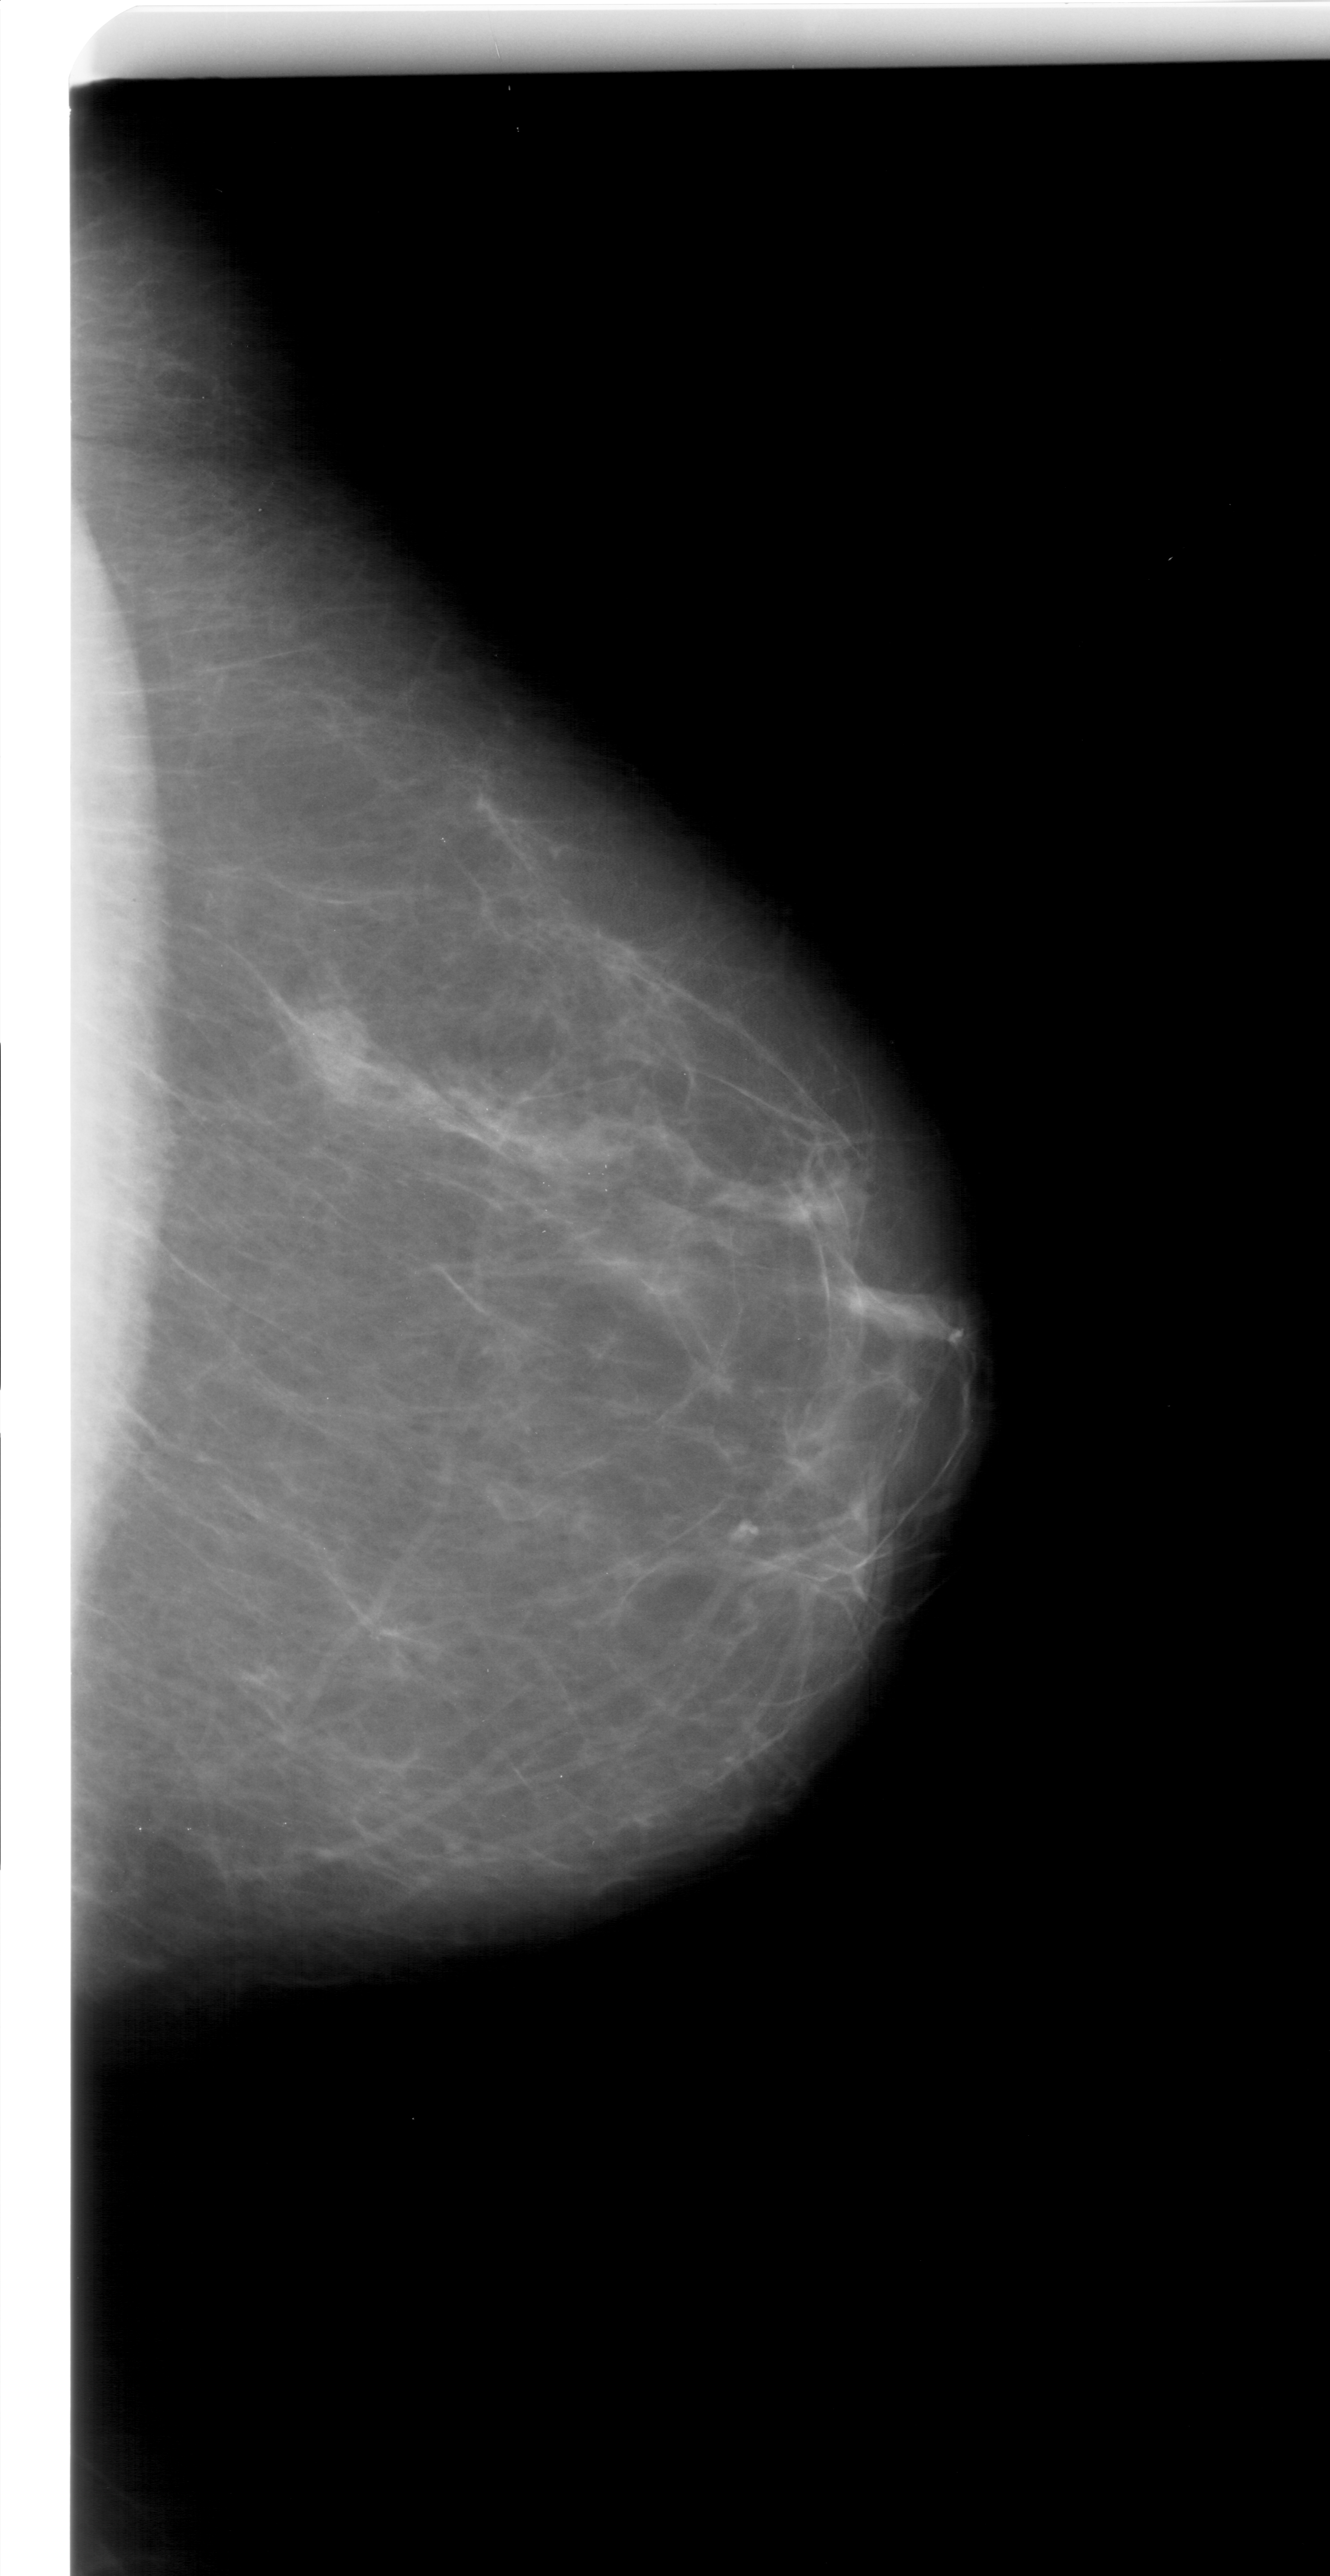
Scanned film-screen mammogram; right breast; craniocaudal (CC) view; BI-RADS breast density category 2 (scale 1–4); 1330 × 2576 image matrix.
Expert-marked regions of interest on this image (one box per marked abnormality):
- mass, shape focal asymmetric density, margins ill defined; BI-RADS assessment category 4; pathology (as recorded): benign: bounding box [x1, y1, x2, y2] px = [291, 1004, 378, 1105]